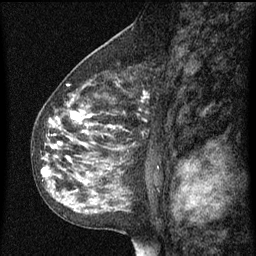
Breast MRI (dynamic contrast-enhanced), one sagittal slice. Slice 42 of 60 in the series (ordered by position). Dynamic contrast-enhanced series, image 2 of 3 at this slice position (ordered by acquisition). 1.5 T. TE 4.2 ms, TR 8 ms. 256 × 256 image matrix, field of view 180 × 180 mm. Patient: female, 55 years.
Structures marked on this image (semi-automatic segmentation, software-assisted and operator-edited):
- analysis volume of interest (the breast-tissue region the enhancement analysis was run in; not a lesion): box from (x=34, y=68) to (x=153, y=151) px
- tumour enhancement mask (voxels above the 70 % enhancement threshold inside the analysis volume of interest): (x=46, y=86)–(x=149, y=151)